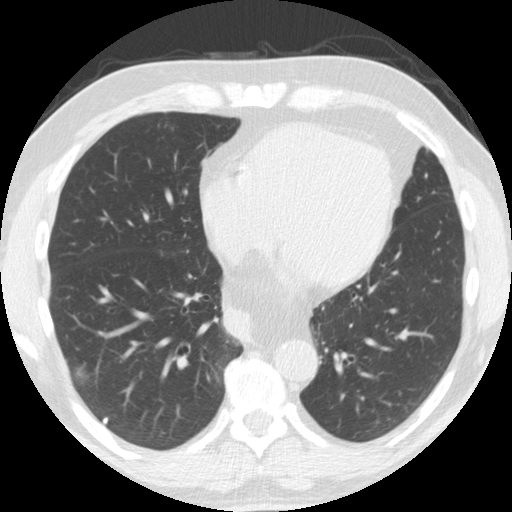
Low-dose screening chest CT, axial slice, second annual screen, lung window (W 1500 / L -600 HU), standard (soft-tissue) reconstruction kernel (STANDARD), 120 kVp, slice 108 of 174 in the series, 512 × 512 image matrix. Male participant, aged 61 years at enrolment.
- Expert reader's lesion annotation, bounding box [x1, y1, x2, y2] px = [41, 319, 110, 398].
- Screening reader's record for this exam (one nodule recorded; not confirmed to be the boxed lesion): non-calcified nodule or mass ≥4 mm, right lower lobe, 33 × 19 mm, smooth margins, soft tissue attenuation, pre-existing on the prior screen: yes; interval growth: yes.
- Lung cancer was diagnosed 30 days after this screen: adenosquamous carcinoma, right lower lobe, poorly differentiated (G3), stage IV (AJCC 6th edition), 45 mm at pathology.